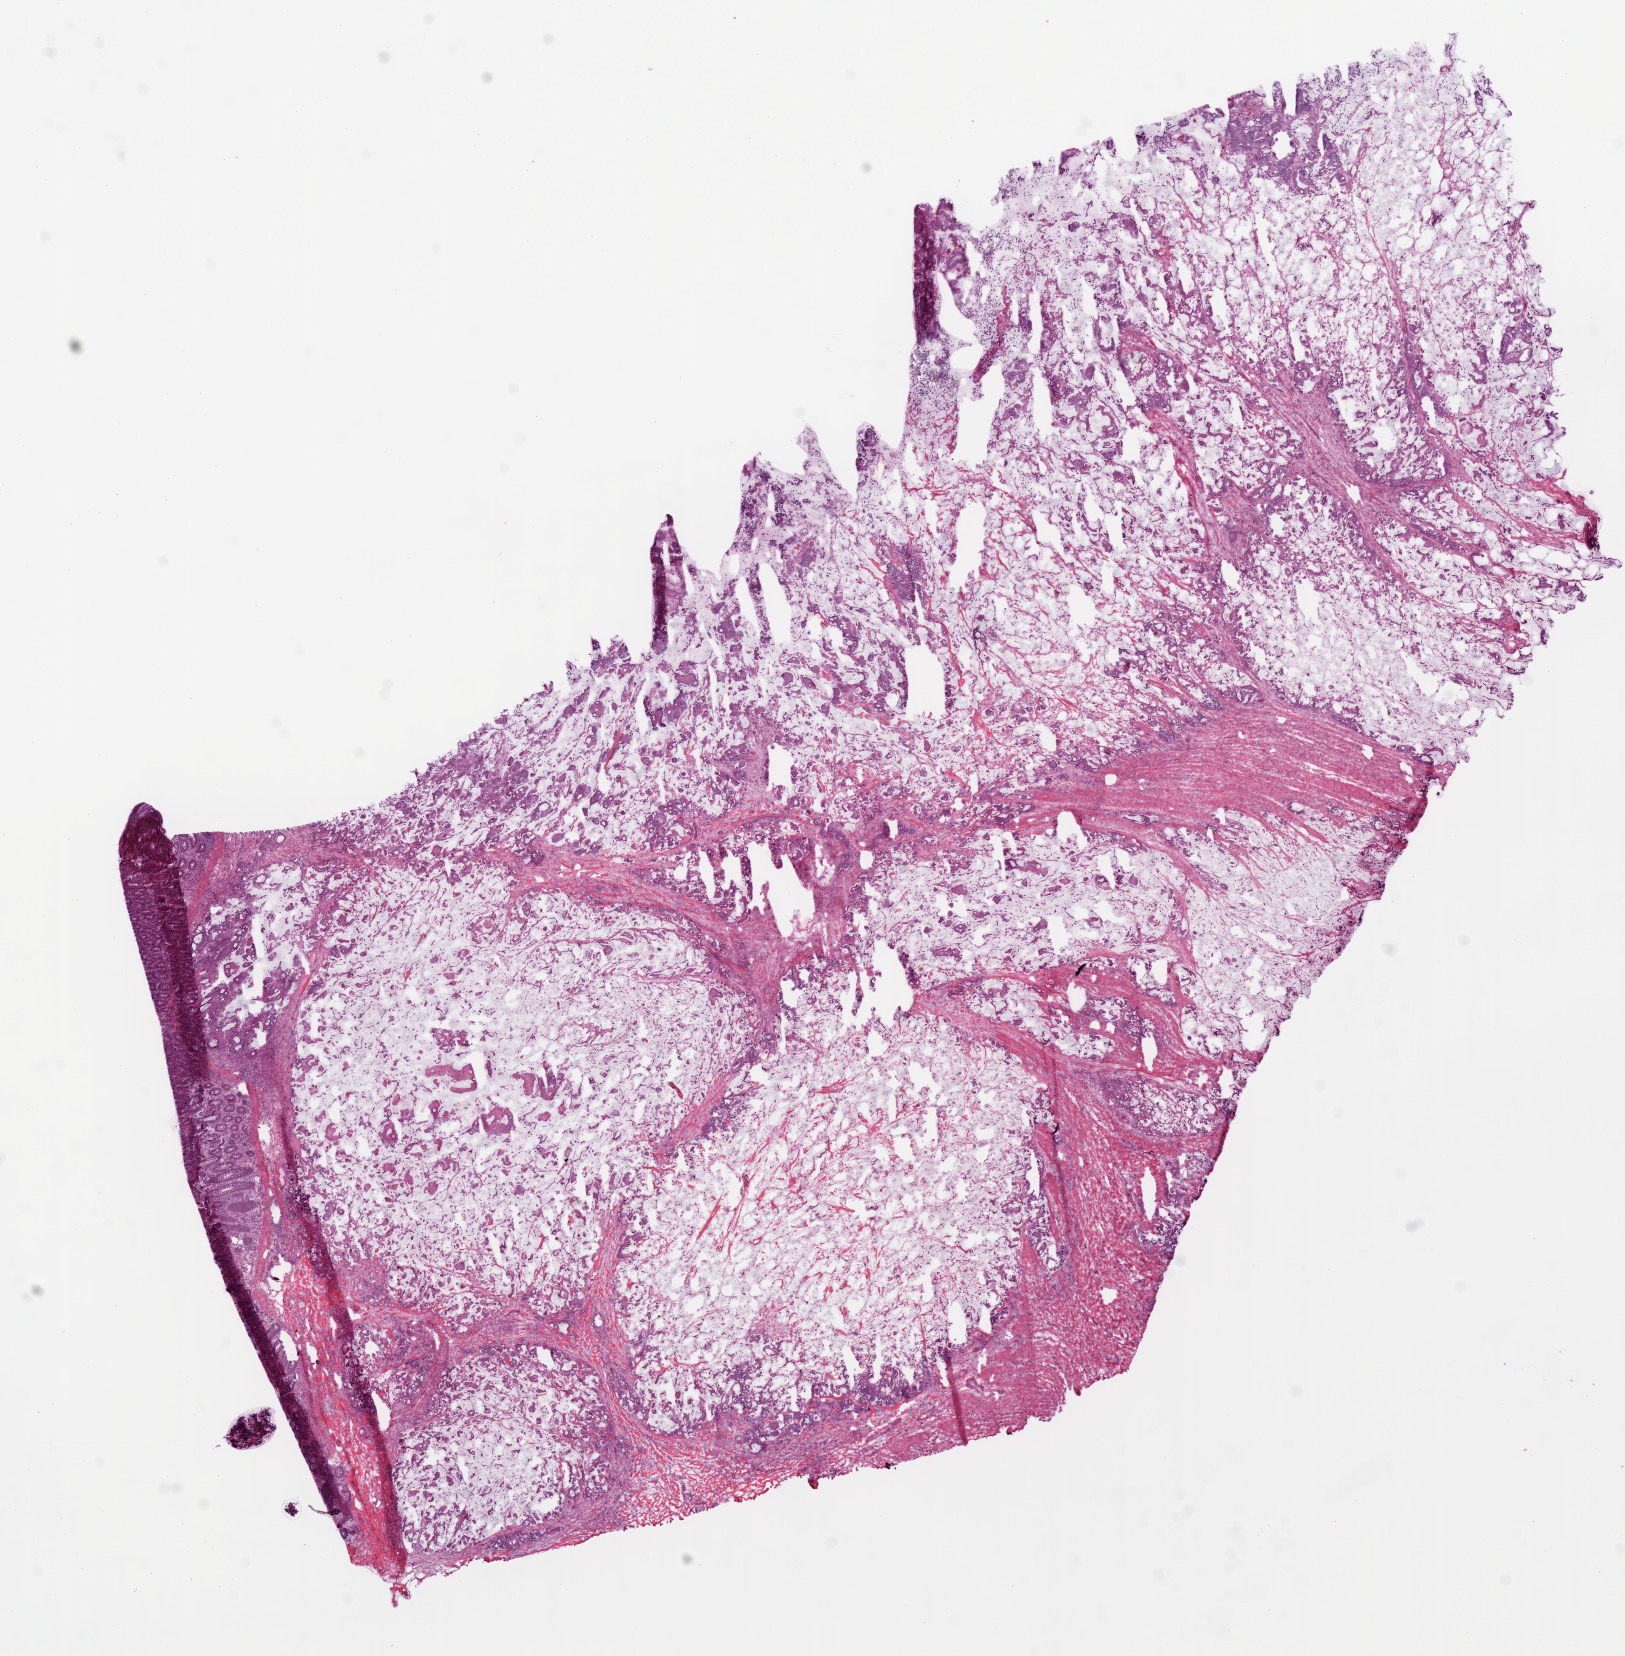
Digitized H&E-stained tissue section (whole slide) — shown as a low-resolution overview of the whole scanned area (about 13.0 x 13.3 mm, from a 20x scan); frozen section from the bottom of the tissue portion; sample: primary tumour, colon. Patient: female, age at initial diagnosis 64 years. Composition of this section per pathologist review: tumour cells 83%, tumour nuclei 70%, normal cells 2%, stromal cells 15%, necrosis 0%.
• AJCC pathologic stage: IV
• lymph nodes positive (case pathology): 9 of 10 examined
• pathologic diagnosis: Mucinous adenocarcinoma (cecum)